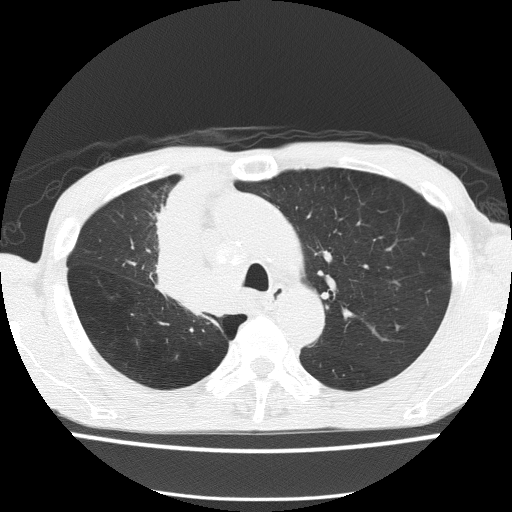
Low-dose screening chest CT, axial slice. Baseline screening round. Lung window (W 1500 / L -600 HU). 2 mm slice thickness. 120 kVp. 512 × 512 image matrix. Male participant, aged 59 years at enrolment.
Expert reader's lesion annotation, bounding box <136,232,236,324> (left, top, right, bottom; pixels). The screening reader recorded 5 non-calcified nodules or masses ≥4 mm on this exam (left upper lobe, left upper lobe, left upper lobe, right middle lobe, right lower lobe); which of them this box marks is not recorded. Official screen result: positive, change unspecified: nodule(s) >= 4 mm or enlarging nodule(s), mass(es), or other non-specific abnormalities suspicious for lung cancer. Participant outcome: lung cancer diagnosed 72 days after this screen — squamous cell carcinoma, NOS, right upper lobe, moderately differentiated (G2), stage IV (AJCC 6th edition).